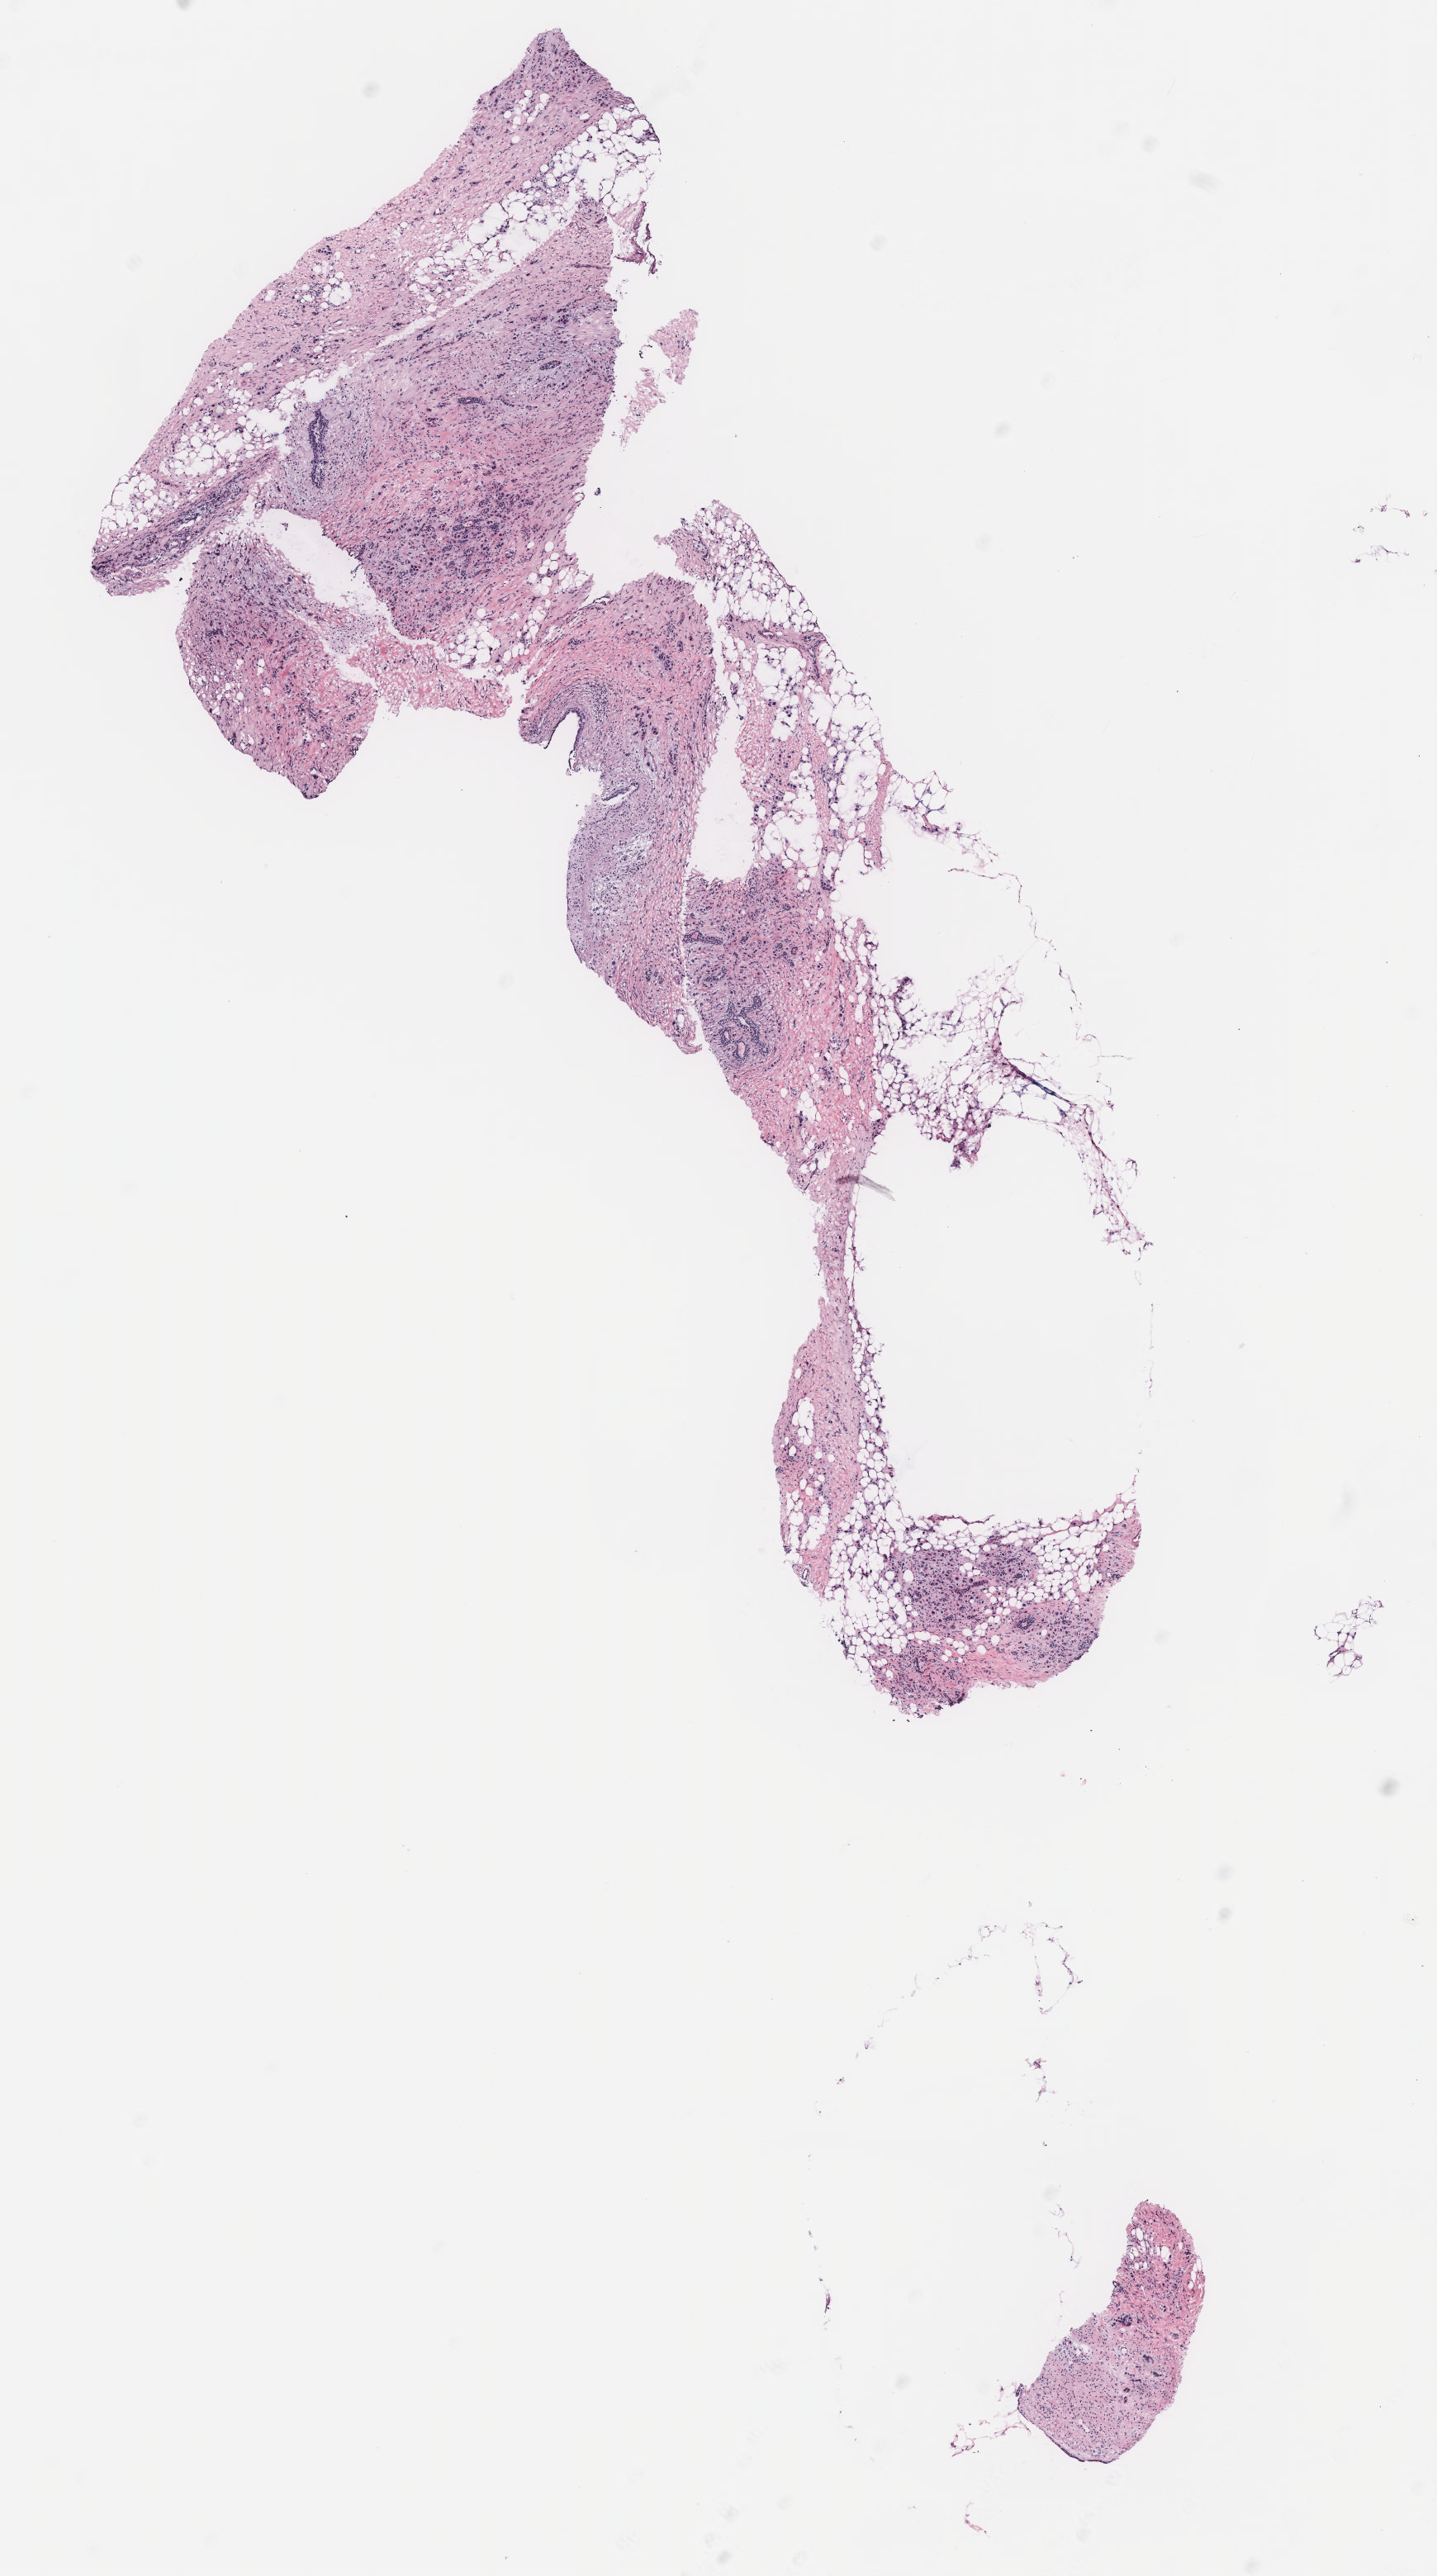
Digitized H&E-stained tissue section (whole slide) — a low-resolution overview of the entire scanned area, about 7.0 x 12.5 mm (from a 40x scan). Tumour tissue sample, breast. Female, 51 y/o.
Histologic diagnosis: Infiltrating duct carcinoma, NOS.